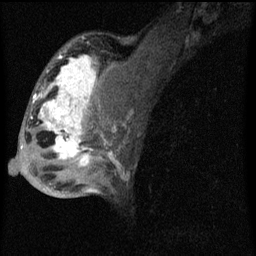
Breast MRI (dynamic contrast-enhanced), one sagittal slice; slice 37 of 60 in the series (ordered by position); dynamic contrast-enhanced series, image 2 of 4 at this slice position (ordered by acquisition); 1.5 T; TE 4.2 ms, TR 8 ms; 2 mm slice thickness; 256 × 256 image matrix, field of view 180 × 180 mm. Patient: female, 50 years.
Outlined on this slice (semi-automatic segmentation, software-assisted and operator-edited):
- analysis volume of interest (the breast-tissue region the enhancement analysis was run in; not a lesion): bounding box (x1, y1, x2, y2) in pixels: (26, 44, 124, 177)
- tumour enhancement mask (voxels above the 70 % enhancement threshold inside the analysis volume of interest): (32, 54, 106, 167)